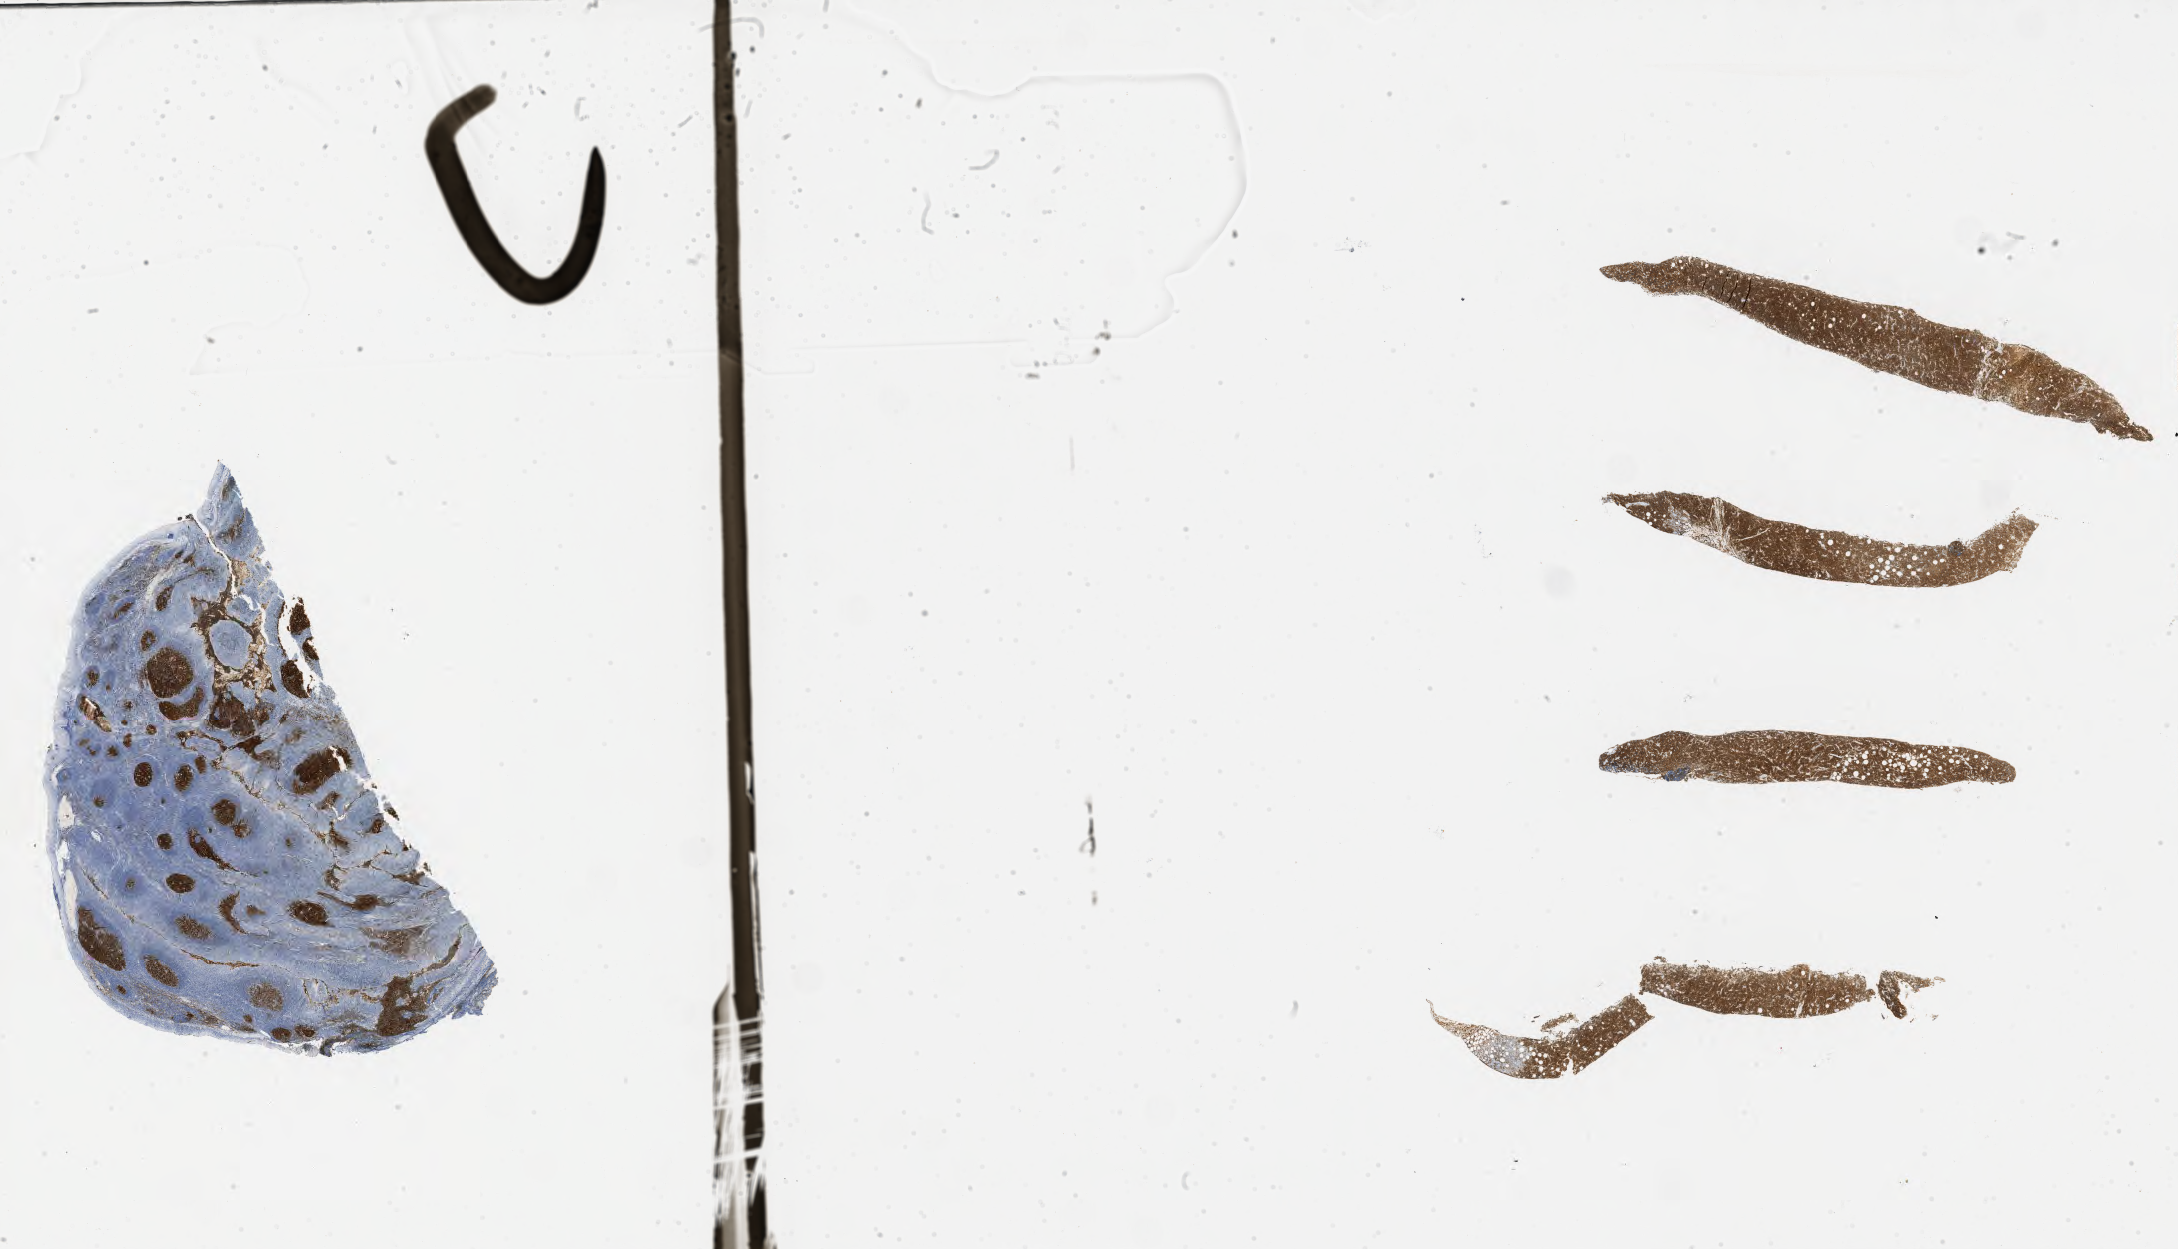
IHC for CD10, whole-slide image, shown as a low-resolution overview of the whole scanned area (about 35.2 x 20.2 mm); tumor tissue. Patient: male, 69 years old.
- histologic diagnosis: Diffuse large B-cell lymphoma, NOS